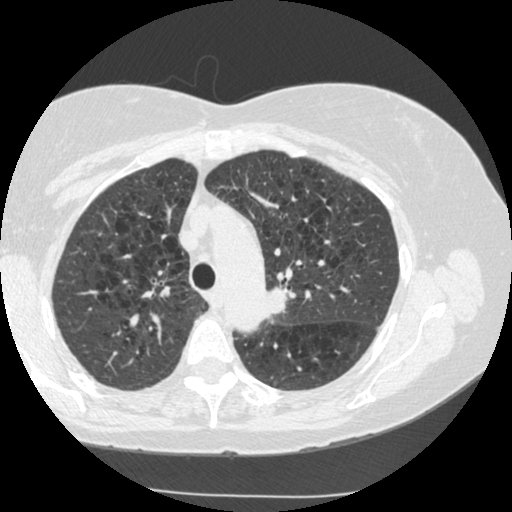
Chest CT (low-dose screening protocol), one axial image. Second annual screen. Lung window (W 1500 / L -600 HU). 1.25 mm slice thickness. Female participant, aged 70 years at enrolment. Current smoker at enrolment.
Lesion marked by an expert reader, box from (x=243, y=268) to (x=309, y=331) px. The exam's reader record, not a measurement of the box and not confirmed to be the same lesion: non-calcified nodule or mass ≥4 mm, left upper lobe, 15 × 13 mm, spiculated (stellate) margins, soft tissue attenuation, pre-existing on the prior screen: yes; interval growth: yes. Official screen result: positive, other. Participant outcome: lung cancer diagnosed 360 days after this screen (after the third annual screen) — neoplasm, malignant, left upper lobe, stage IIIB (AJCC 6th edition), 40 mm at pathology.